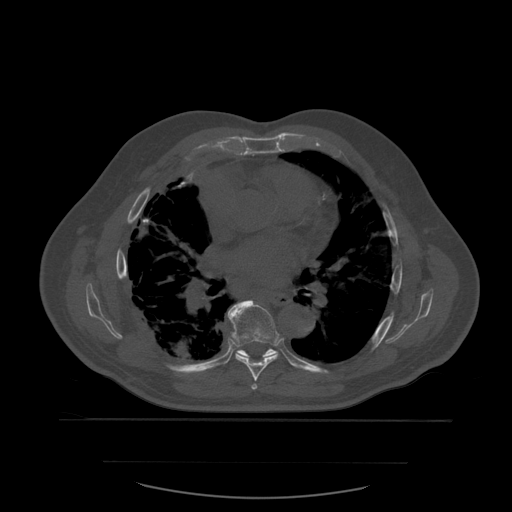
CT including the spine, one axial slice. Position 378 of 590 along the scan axis. Bone window (W 1800 / L 400 HU). 1.25 mm slice thickness. 512 × 512 image matrix, field of view 479 × 479 mm. Patient age 71 years. From the clinical record (not read from this slice): primary cancer: lung; vertebrae with lytic lesions (as recorded): T1, T2, L5, S1.
Annotated regions visible in this slice (semi-automatically segmented with operator editing):
- T6 vertebra: bounding box (x1, y1, x2, y2) in pixels: (252, 384, 258, 390)
- T7 vertebra: (228, 300, 280, 382)
- T8 vertebra: (229, 314, 276, 360)